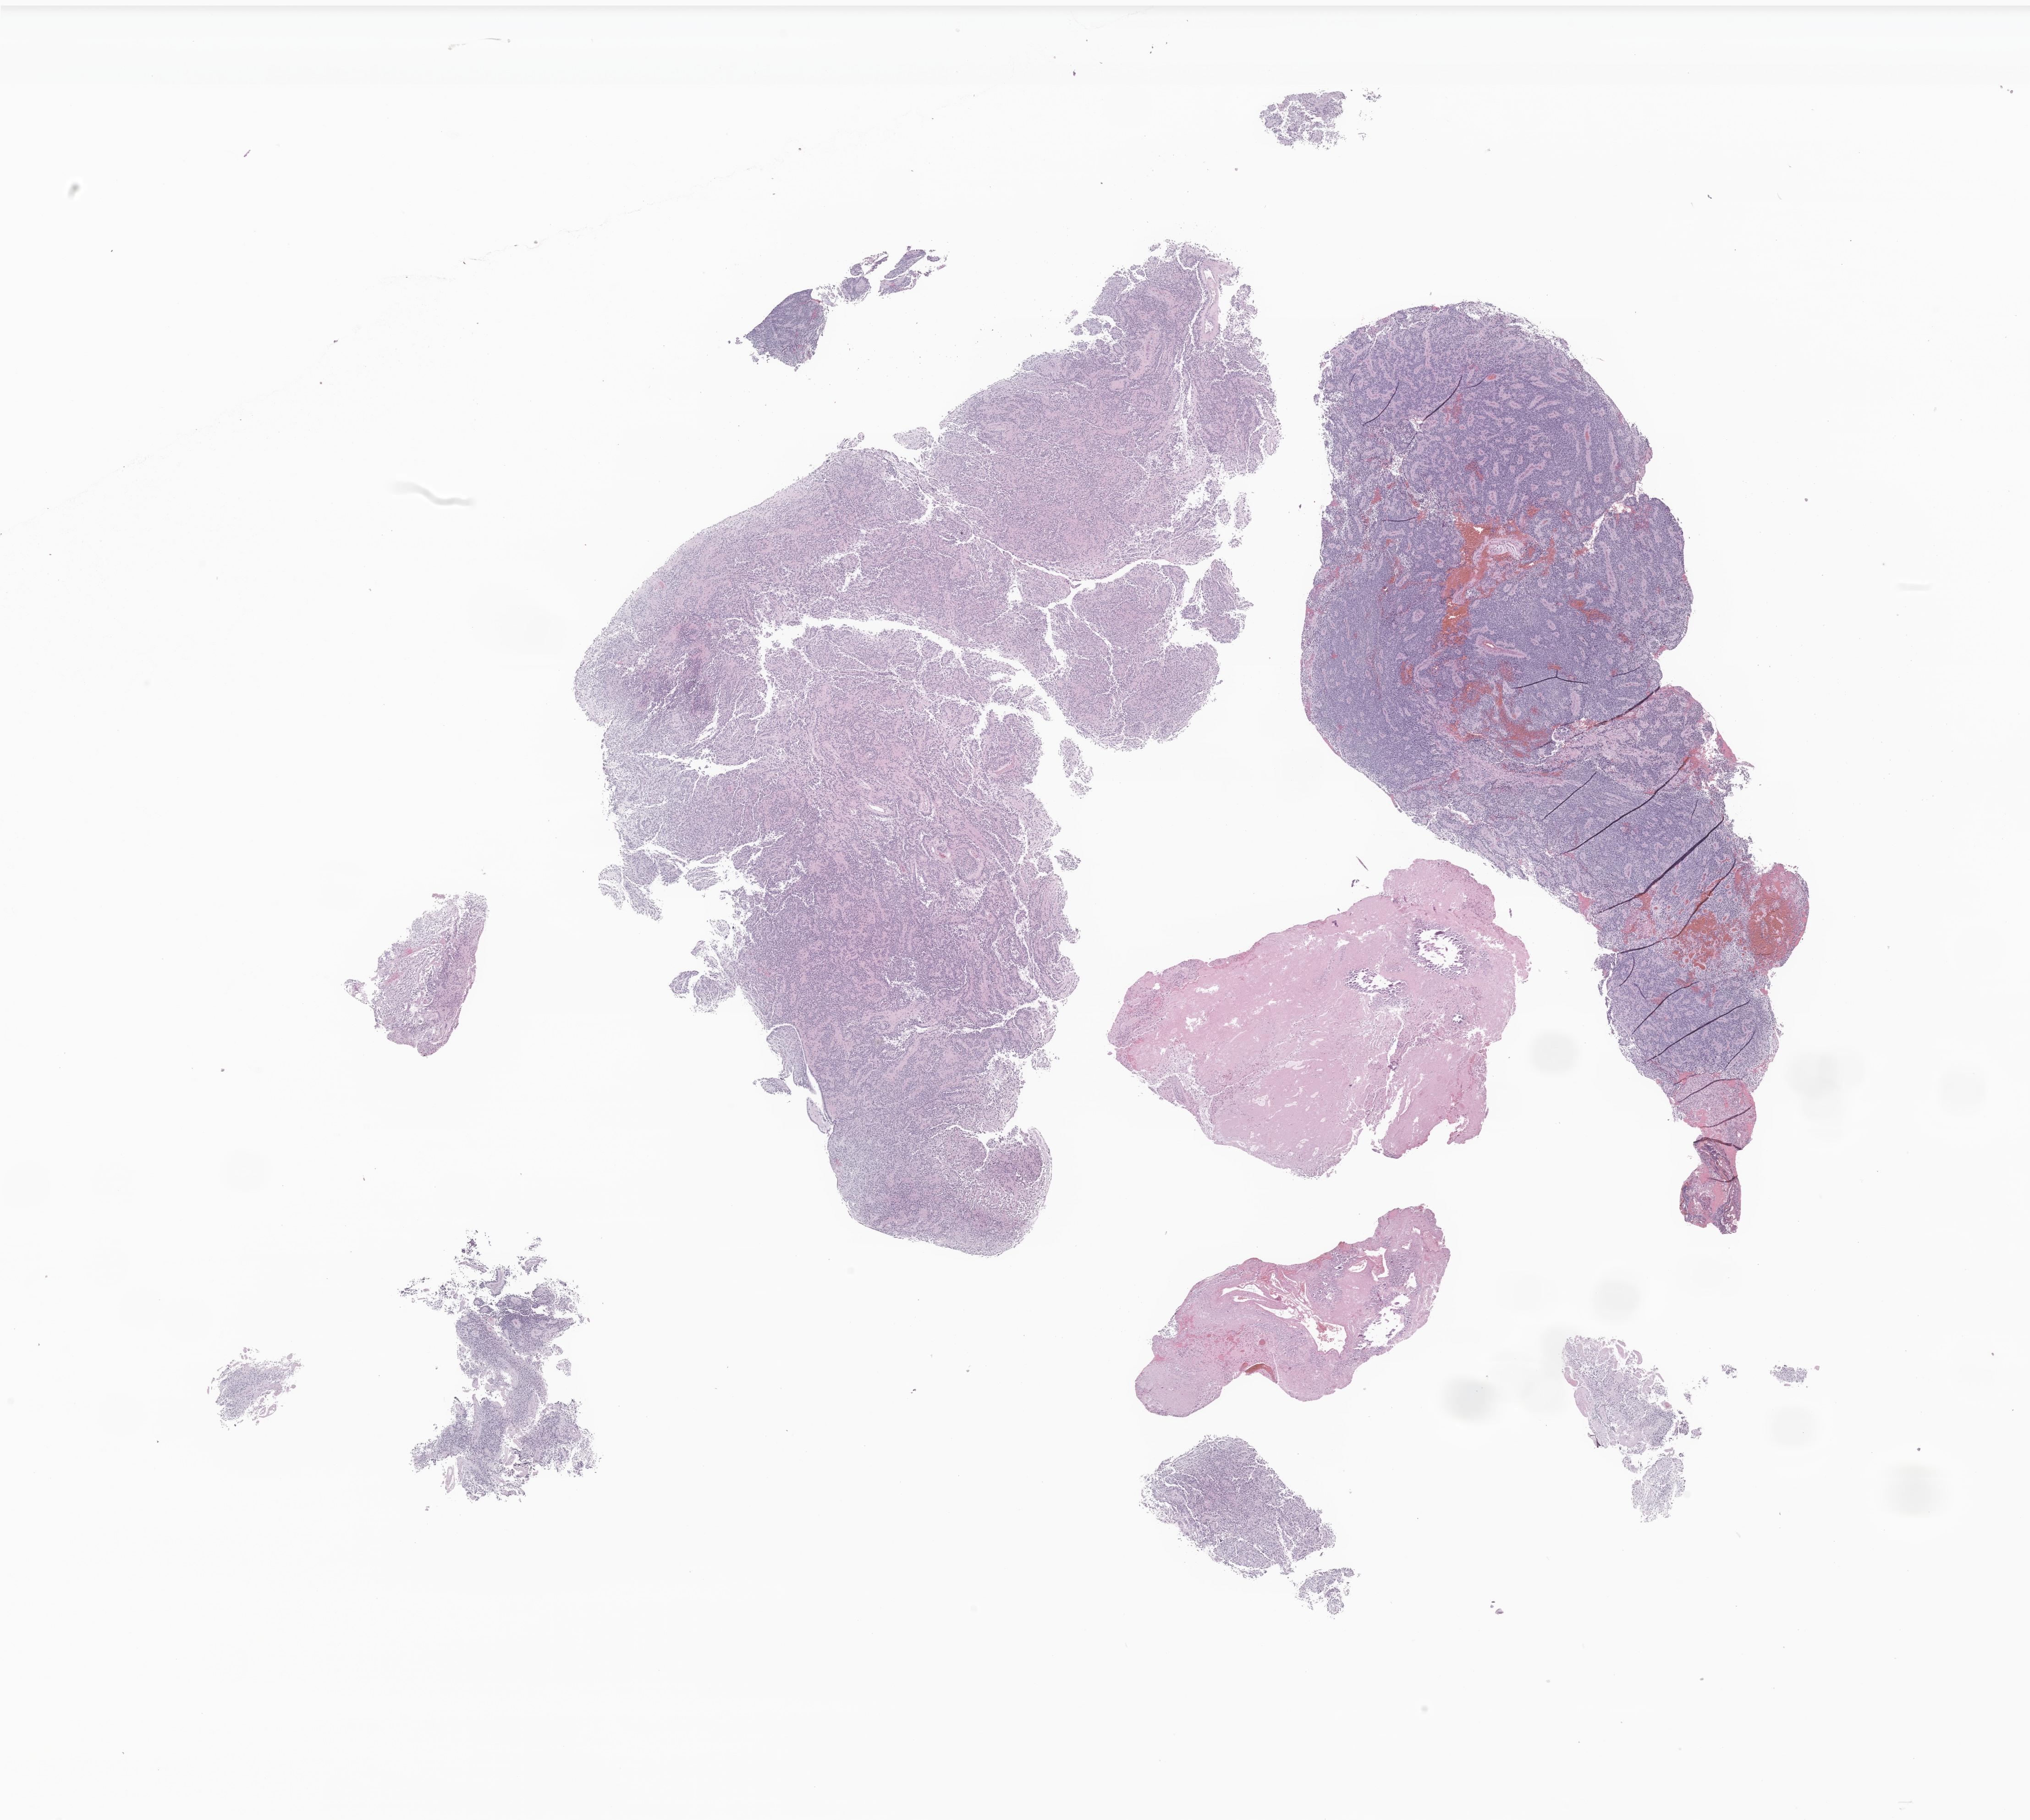
Digitized hematoxylin and eosin (H&E)-stained section of tumor tissue from the brain, whole scanned area (about 18.7 x 16.7 mm) shown as a low-resolution overview; formalin-fixed paraffin-embedded section. Patient: female, age 774 days (about 2.1 years).
Diagnosis (ICD-O-3 morphology term): Ependymoma, anaplastic.